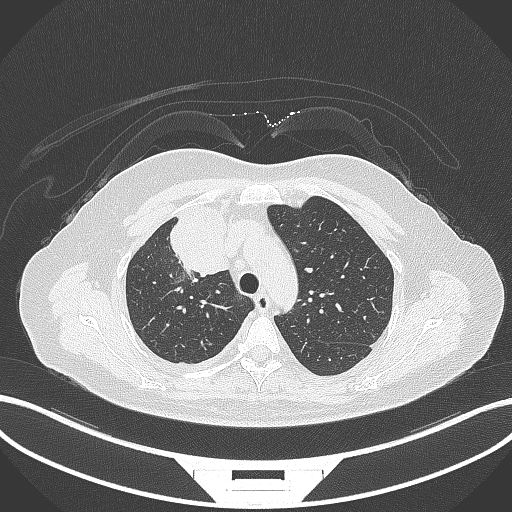
Chest CT, one axial slice; position 223 of 305 along the scan axis; reconstruction kernel B70f; 120 kVp; lung window (W 1500 / L -600 HU); 512 × 512 image matrix, field of view 400 × 400 mm. Patient: female, 52 years. Case-level facts recorded for this patient, not image findings: clinical TNM (as recorded): T3 N1 M1.
Annotated regions visible in this slice (bounding box drawn by a radiologist):
- lung tumour (recorded histology: adenocarcinoma): box from (x=155, y=201) to (x=233, y=277) px